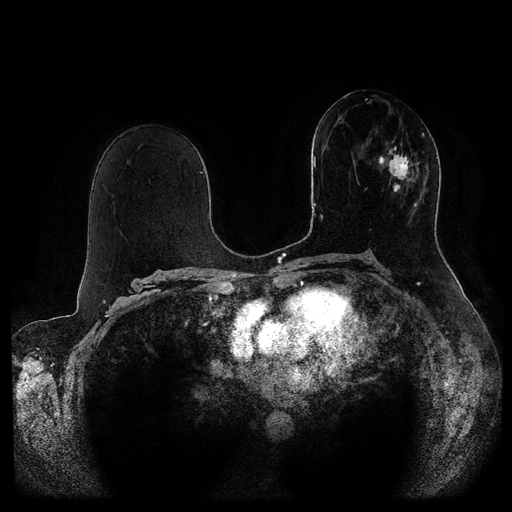
Breast MRI (dynamic contrast-enhanced, multi-phase), one axial slice. Slice 54 of 116 in the series (ordered by position). Dynamic contrast-enhanced series, time point 2 of 5 at this slice position (early post-contrast). 1.5 T. TE 2.6 ms, TR 5.3 ms. 2 mm slice thickness. 512 × 512 image matrix, field of view 370 × 370 mm. Patient: female, 51 years.
Annotated regions visible in this slice (semi-automatically segmented with operator editing):
- breast lesion (labelled 'tumour' in the annotation; benign lesions carry a separate 'benign' label): box from (x=378, y=132) to (x=426, y=207) px